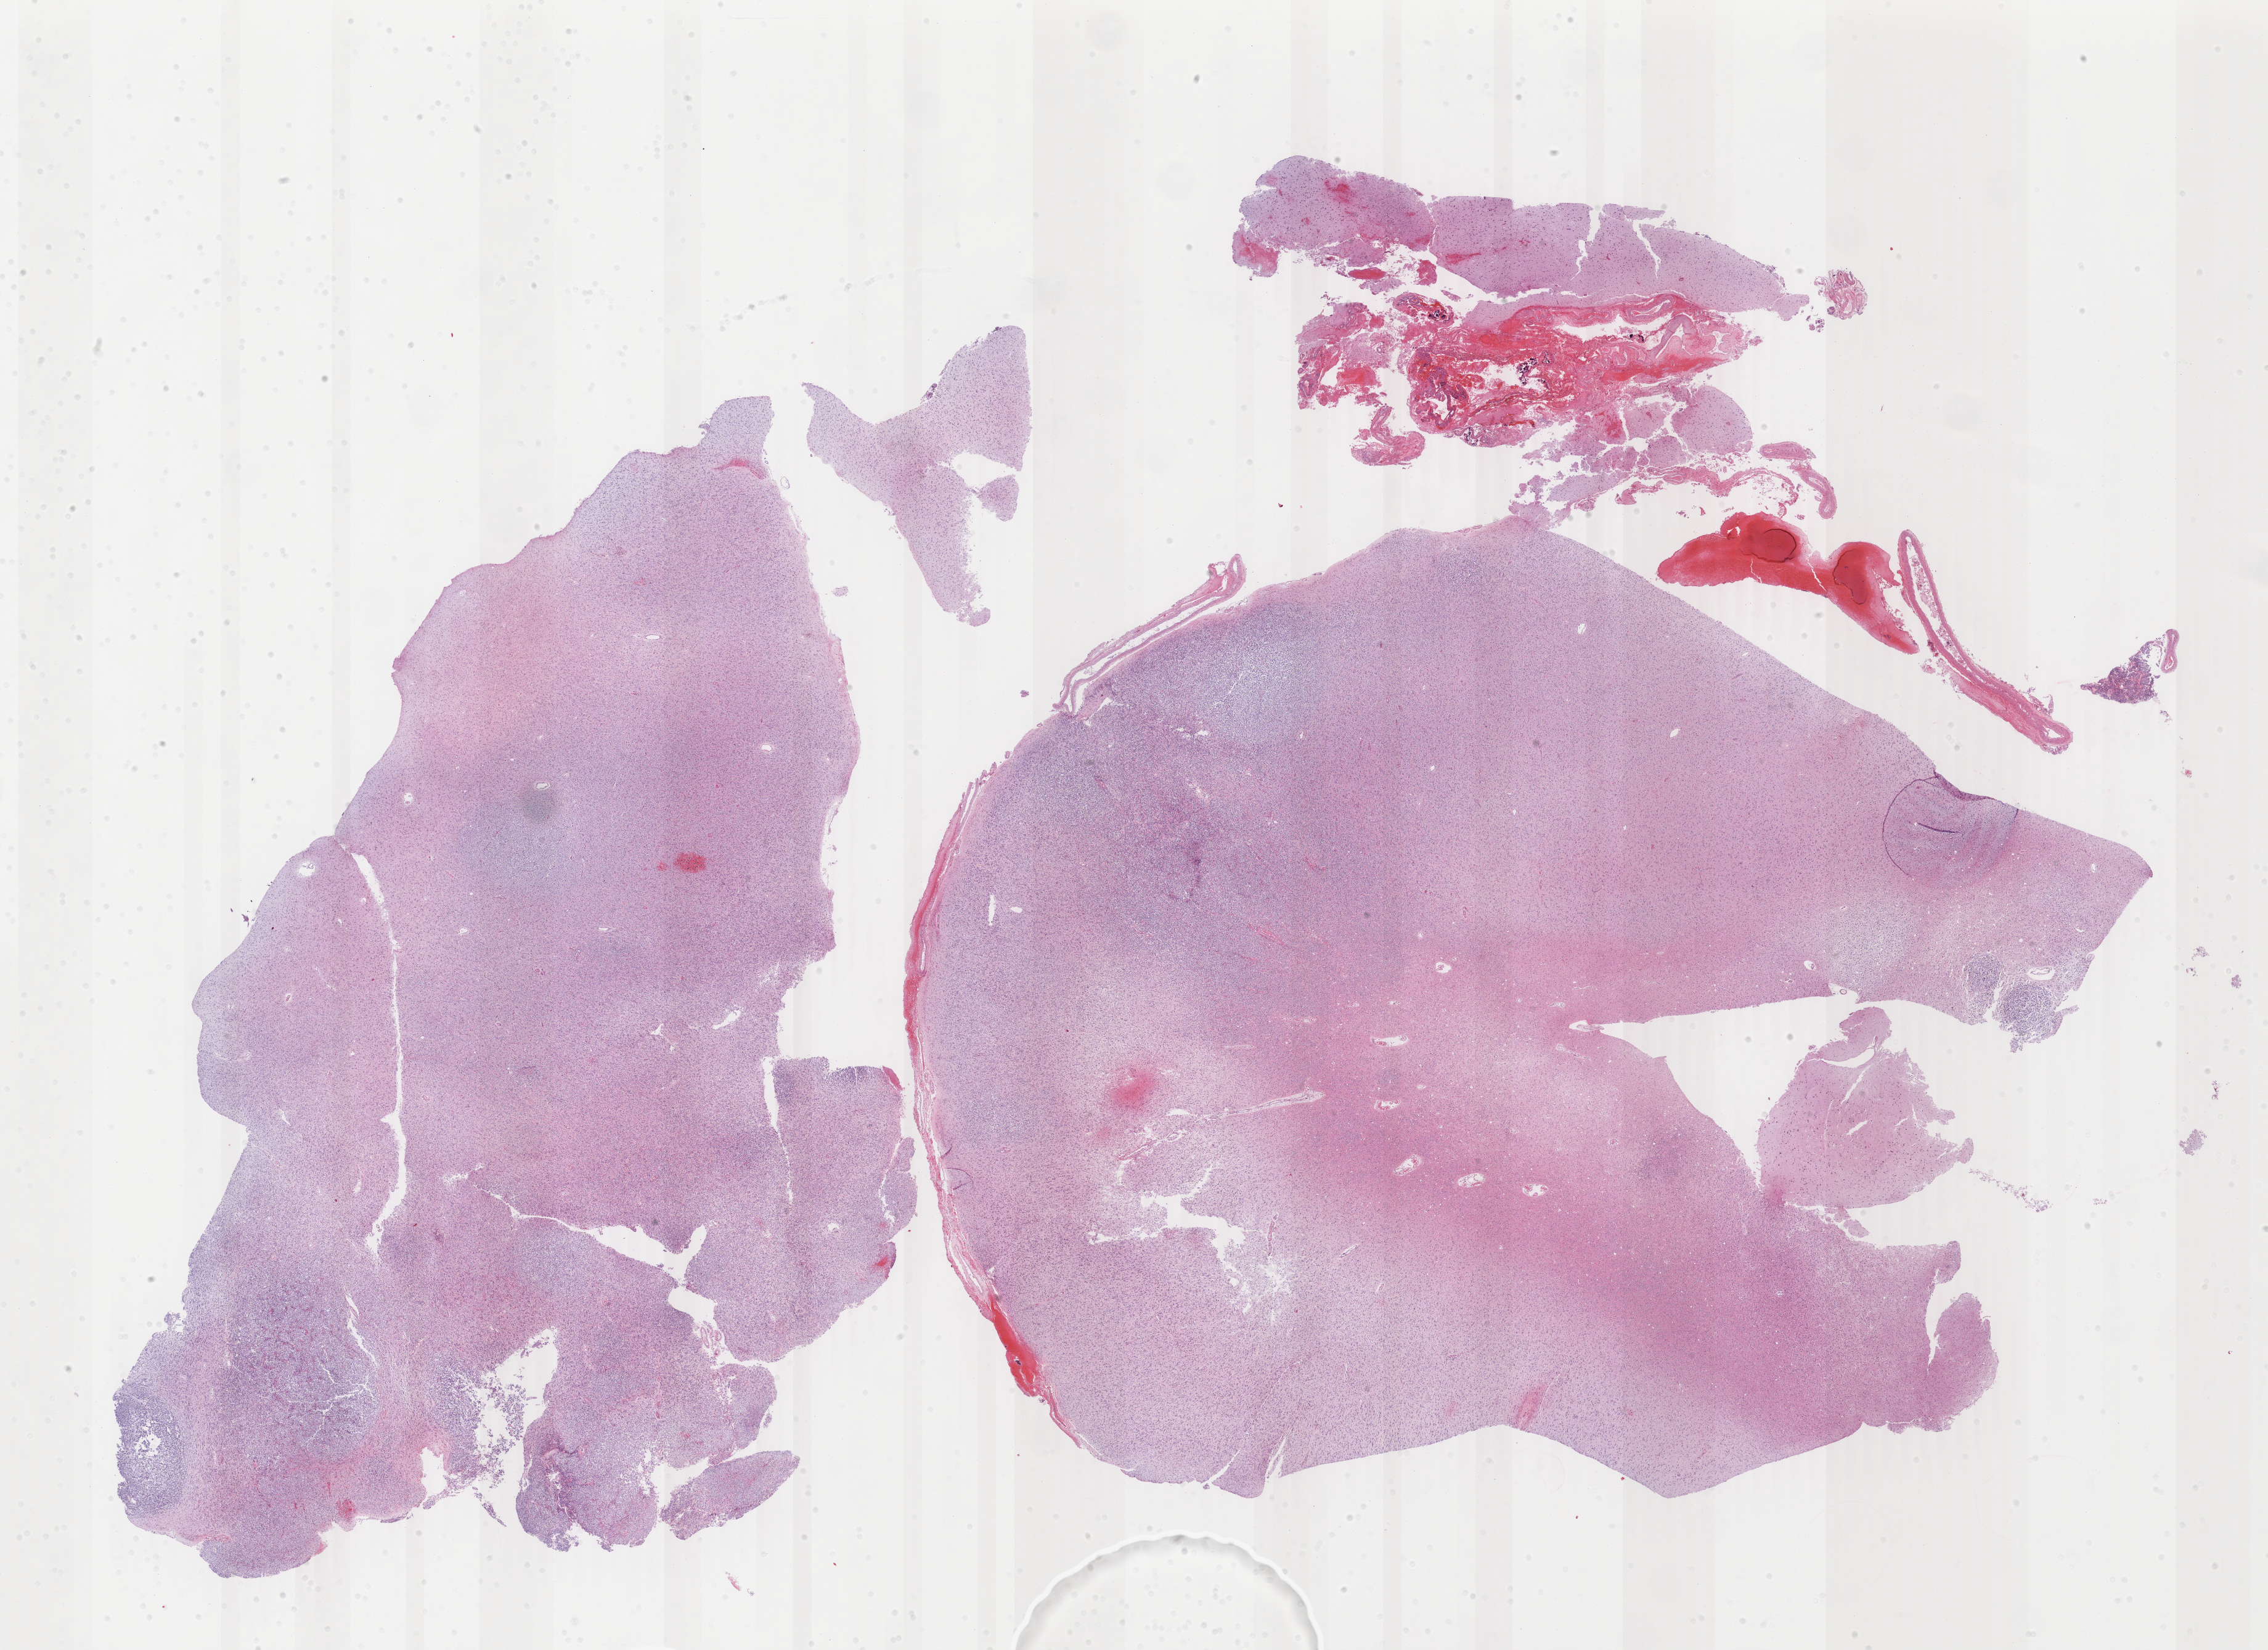
Whole-slide histology image, Hematoxylin and eosin (H&E) stained — a low-resolution overview of the entire scanned area, about 29.3 x 21.3 mm (from a 40x scan); formalin-fixed paraffin-embedded (FFPE) diagnostic section; primary tumour sample from the brain. Patient: female, age at initial diagnosis 56 years. Histologic grade: G3 (poorly differentiated).
Laterality: right. Pathologic diagnosis: Oligodendroglioma, anaplastic (cerebrum).